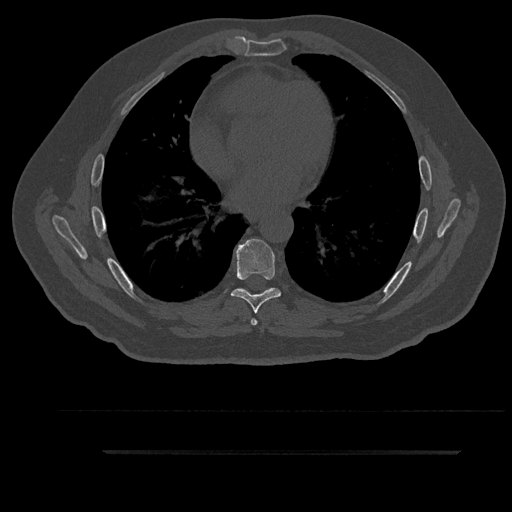
CT including the spine, one axial slice. Slice 524 of 797 in the series (ordered by position). Reconstruction kernel Br40s/3. 120 kVp. Bone window (W 1800 / L 400 HU). 0.5 mm slice thickness. 512 × 512 image matrix, field of view 432 × 432 mm. Male patient, age 63 years. Case-level facts recorded for this patient, not image findings: primary cancer: renal.
Annotated regions visible in this slice (semi-automatic segmentation, software-assisted and operator-edited):
- T6 vertebra: box from (x=251, y=289) to (x=269, y=326) px
- T7 vertebra: (x=231, y=239)–(x=281, y=314)